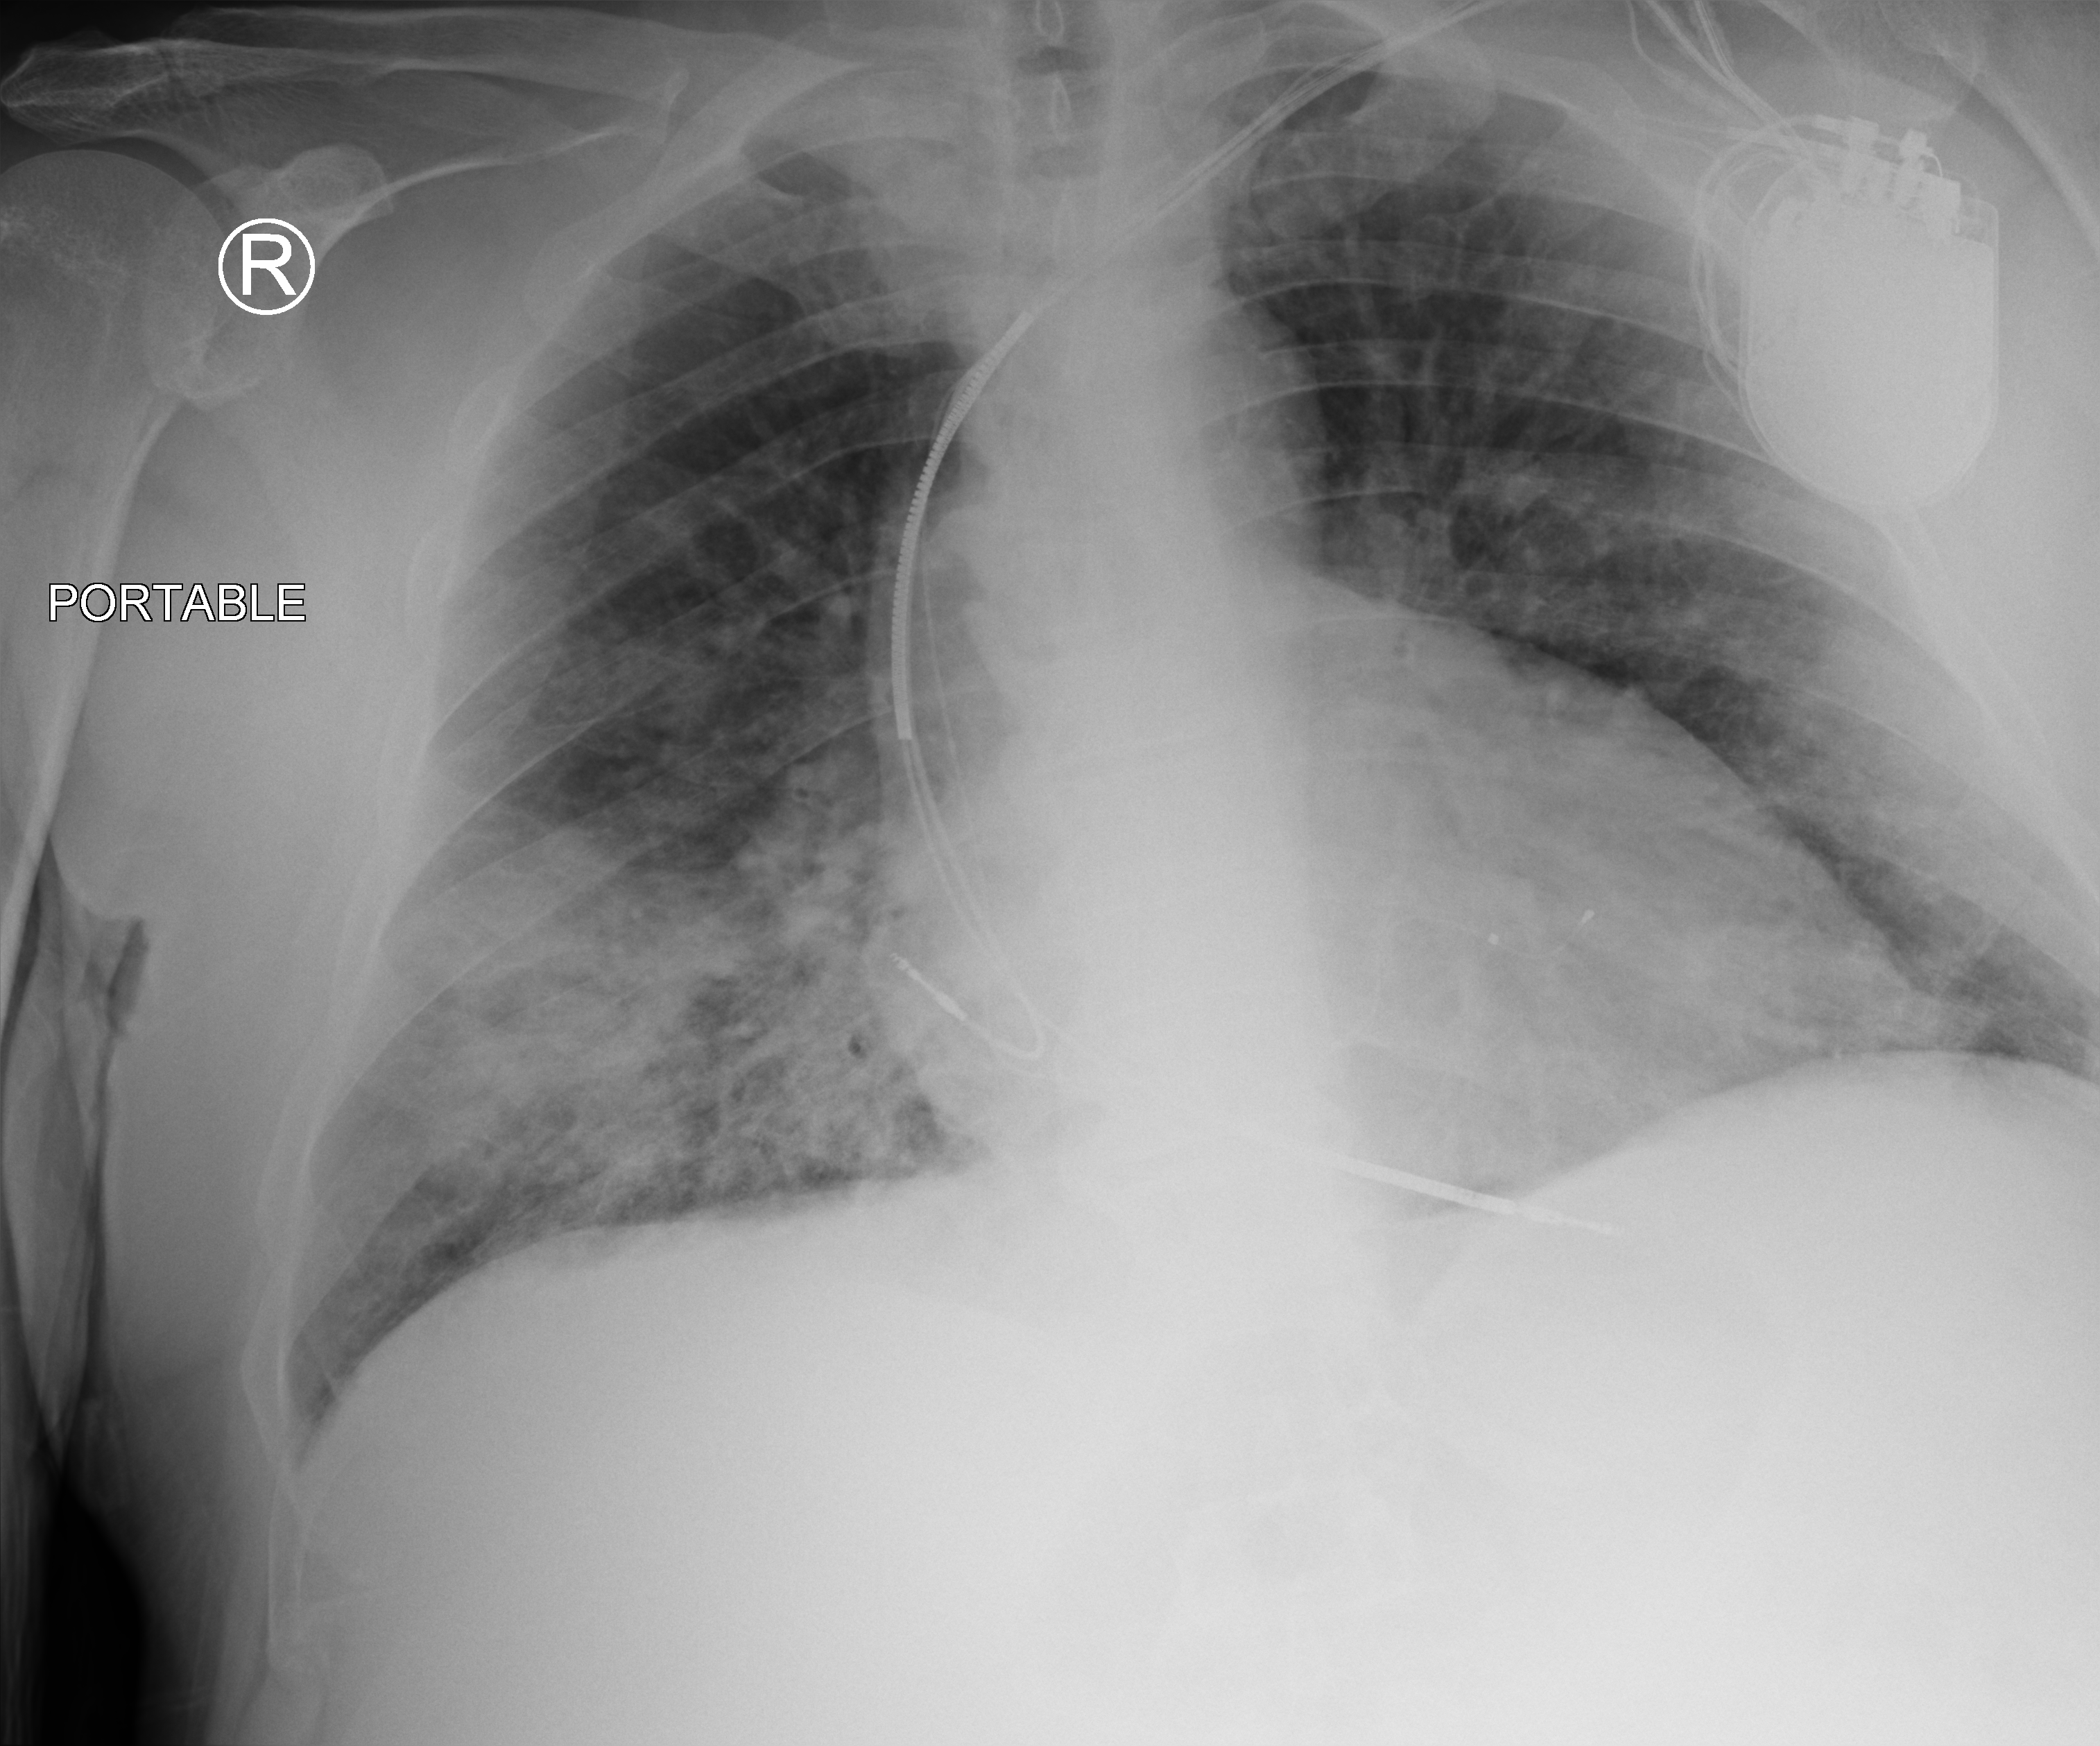
Chest X-ray (portable), anteroposterior (AP) projection. Male patient hospitalised with COVID-19, age 60–74 years.
From the hospital-stay record, not from the radiograph (when in the stay this image was taken is not recorded): other chronic lung disease (admission record): no; chronic kidney disease (admission record): no; COPD (admission record): no.